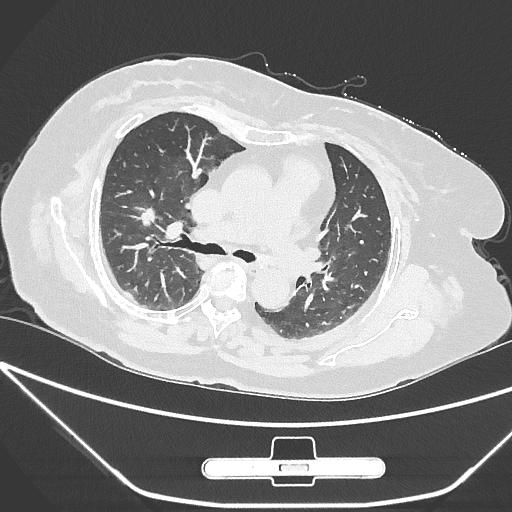
Chest CT, one axial slice. Position 165 of 245 along the scan axis. Lung window (W 1500 / L -600 HU). 512 × 512 image matrix, field of view 365 × 365 mm. Patient: female, 65 years. From the clinical record (not read from this slice): clinical TNM (as recorded): T1c N0 M0; histopathological grade: G3.
Annotated regions visible in this slice (bounding box drawn by a radiologist):
- lung tumour (recorded histology: adenocarcinoma): box from (x=133, y=203) to (x=160, y=234) px